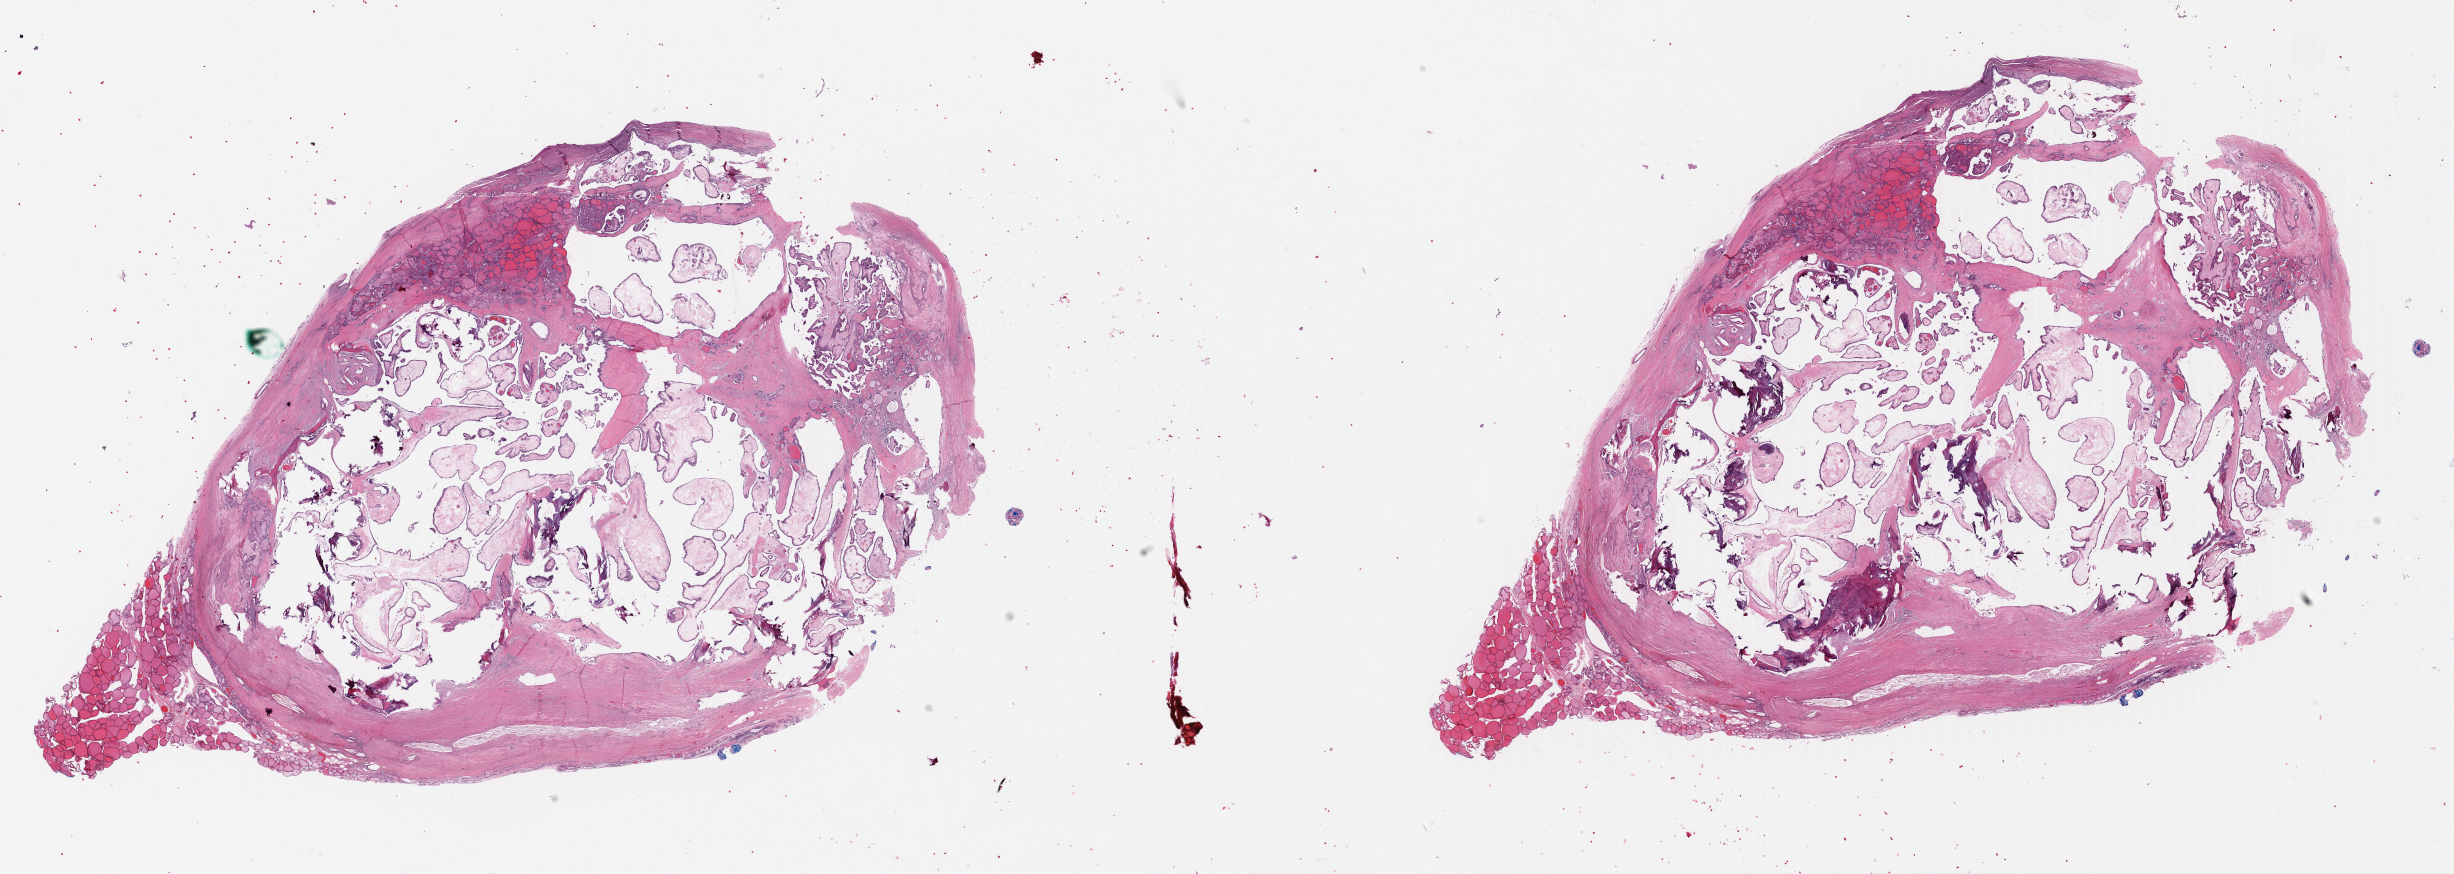
Digitized Hematoxylin and eosin (H&E) stained tissue section (whole slide) — shown as a low-resolution overview of the whole scanned area (about 38.6 x 13.7 mm, from a 40x scan), formalin-fixed paraffin-embedded (FFPE) diagnostic section, thyroid, primary tumour sample. Female, age 70 years at initial diagnosis.
AJCC pathologic stage: I (7th edition). TNM: T1b N0 M0. Diagnosis: Papillary adenocarcinoma, NOS (thyroid gland).